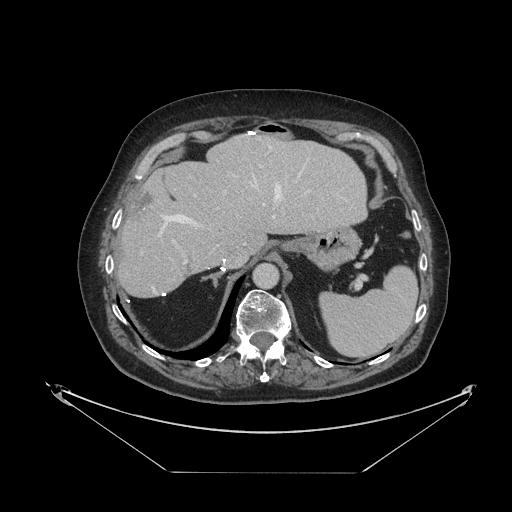
Contrast-enhanced abdominal CT, one axial slice. Slice 78 of 121 in the series (ordered by position). Reconstruction kernel STANDARD. 120 kVp. Soft-tissue window (W 400 / L 40 HU). 2.5 mm slice thickness. 512 × 512 image matrix, field of view 500 × 500 mm. Male patient, age 68 years. From the clinical record (not read from this slice): diagnosis: colorectal cancer liver metastases, imaged before liver resection; multiple liver metastases: no; largest metastasis: 4 cm; disease in both lobes: no.
Structures marked on this image (manually delineated by an expert):
- hepatic veins: bounding box <160,146,310,234> (left, top, right, bottom; pixels)
- liver: <120,136,366,297>
- planned liver remnant (the part of the liver to remain after resection): <120,136,366,296>
- portal vein (with intrahepatic branches): <174,166,261,264>
- liver metastasis: <133,192,152,216>